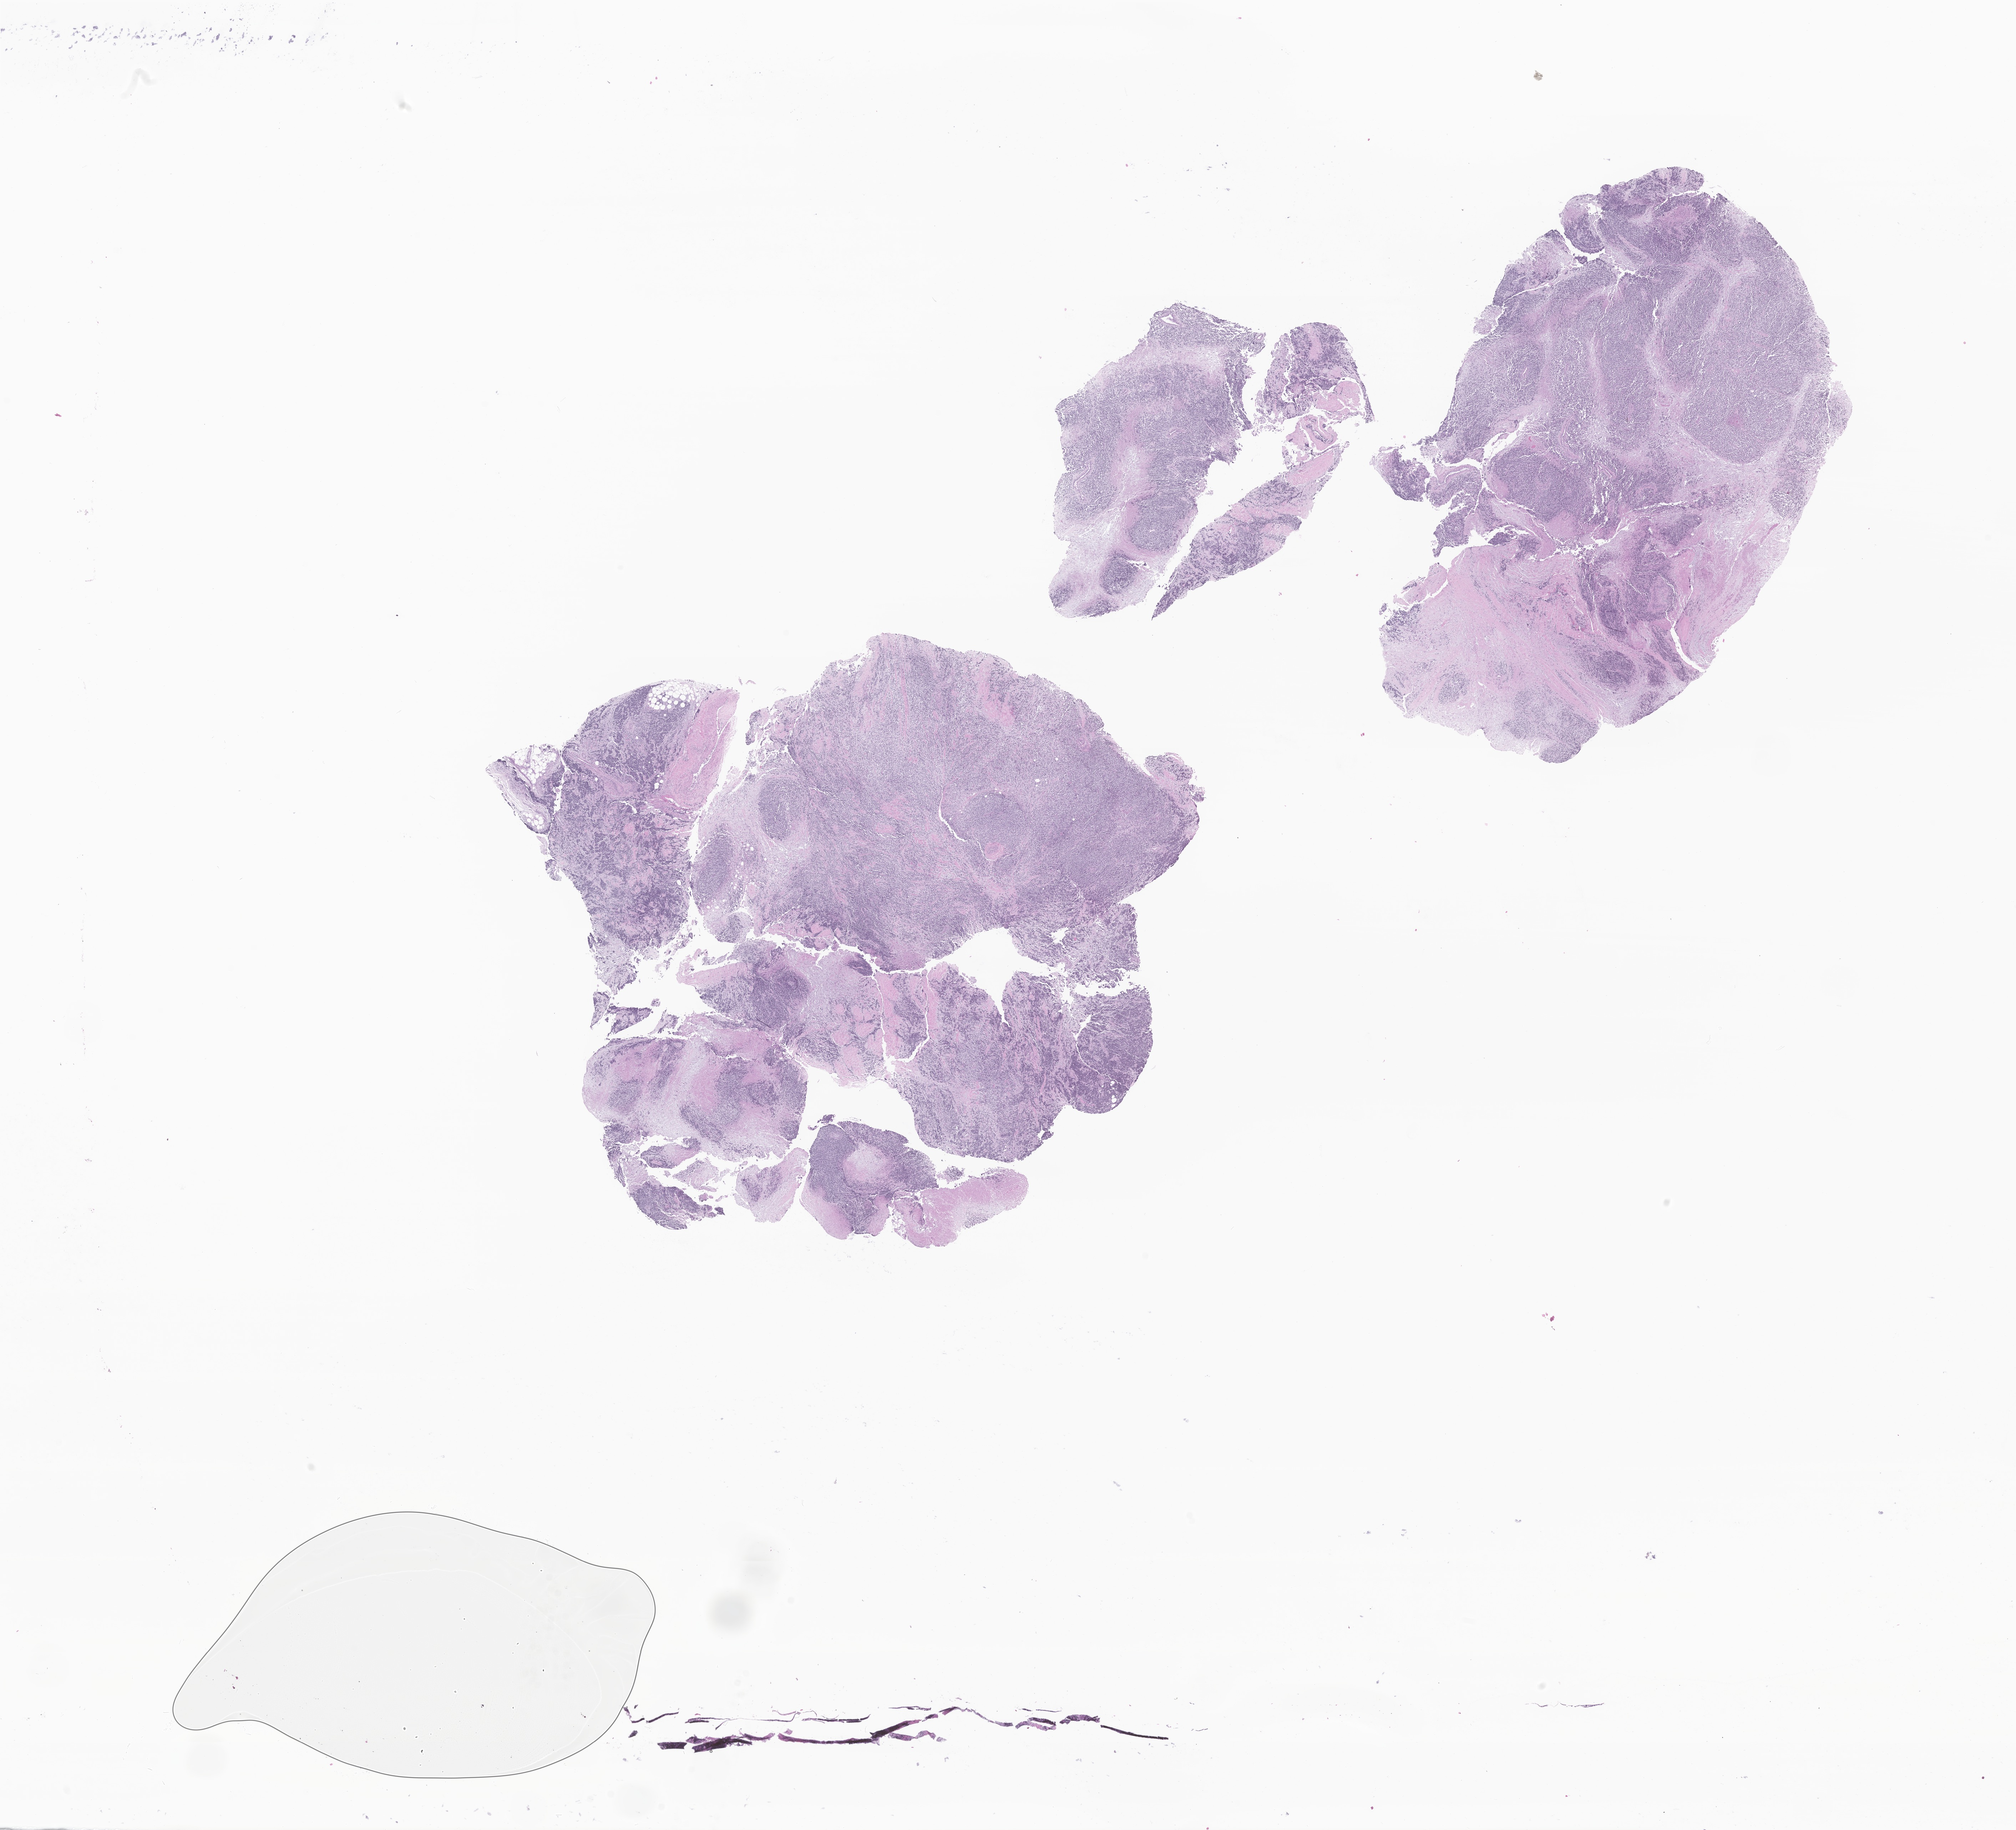
Haematoxylin and eosin whole-slide image of tumor tissue — a low-resolution overview of the entire scanned area, about 23.8 x 21.6 mm, formalin-fixed paraffin-embedded section. Patient male; age 59 months (4 years 11 months).
Diagnosis (ICD-O-3 morphology term): Alveolar rhabdomyosarcoma.